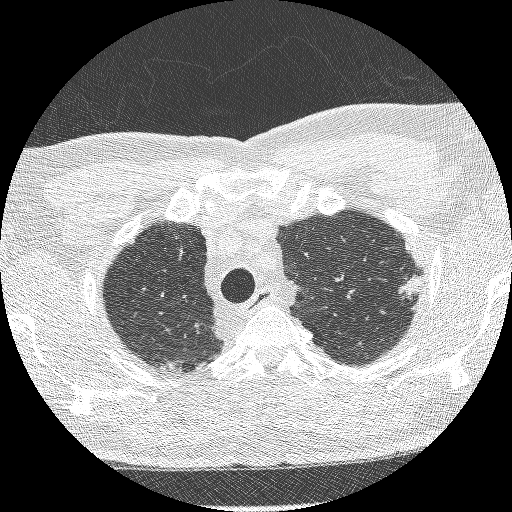
Axial slice from a low-dose chest CT screening exam. Third screening round (two years after baseline). Lung window (W 1500 / L -600 HU). 512 × 512 image matrix. Male participant, aged 66 years at enrolment.
• Expert reader's lesion annotation, box from (x=389, y=269) to (x=433, y=312) px.
• Screening reader's record for this exam (one nodule recorded; not confirmed to be the boxed lesion): non-calcified nodule or mass ≥4 mm, left lower lobe, 15 × 9 mm, spiculated (stellate) margins, soft tissue attenuation, pre-existing on the prior screen: yes; interval growth: yes.
• Lung cancer was diagnosed 225 days after this screen: adenocarcinoma, NOS, left upper lobe, poorly differentiated (G3), stage IB (AJCC 6th edition), 16 mm at pathology.